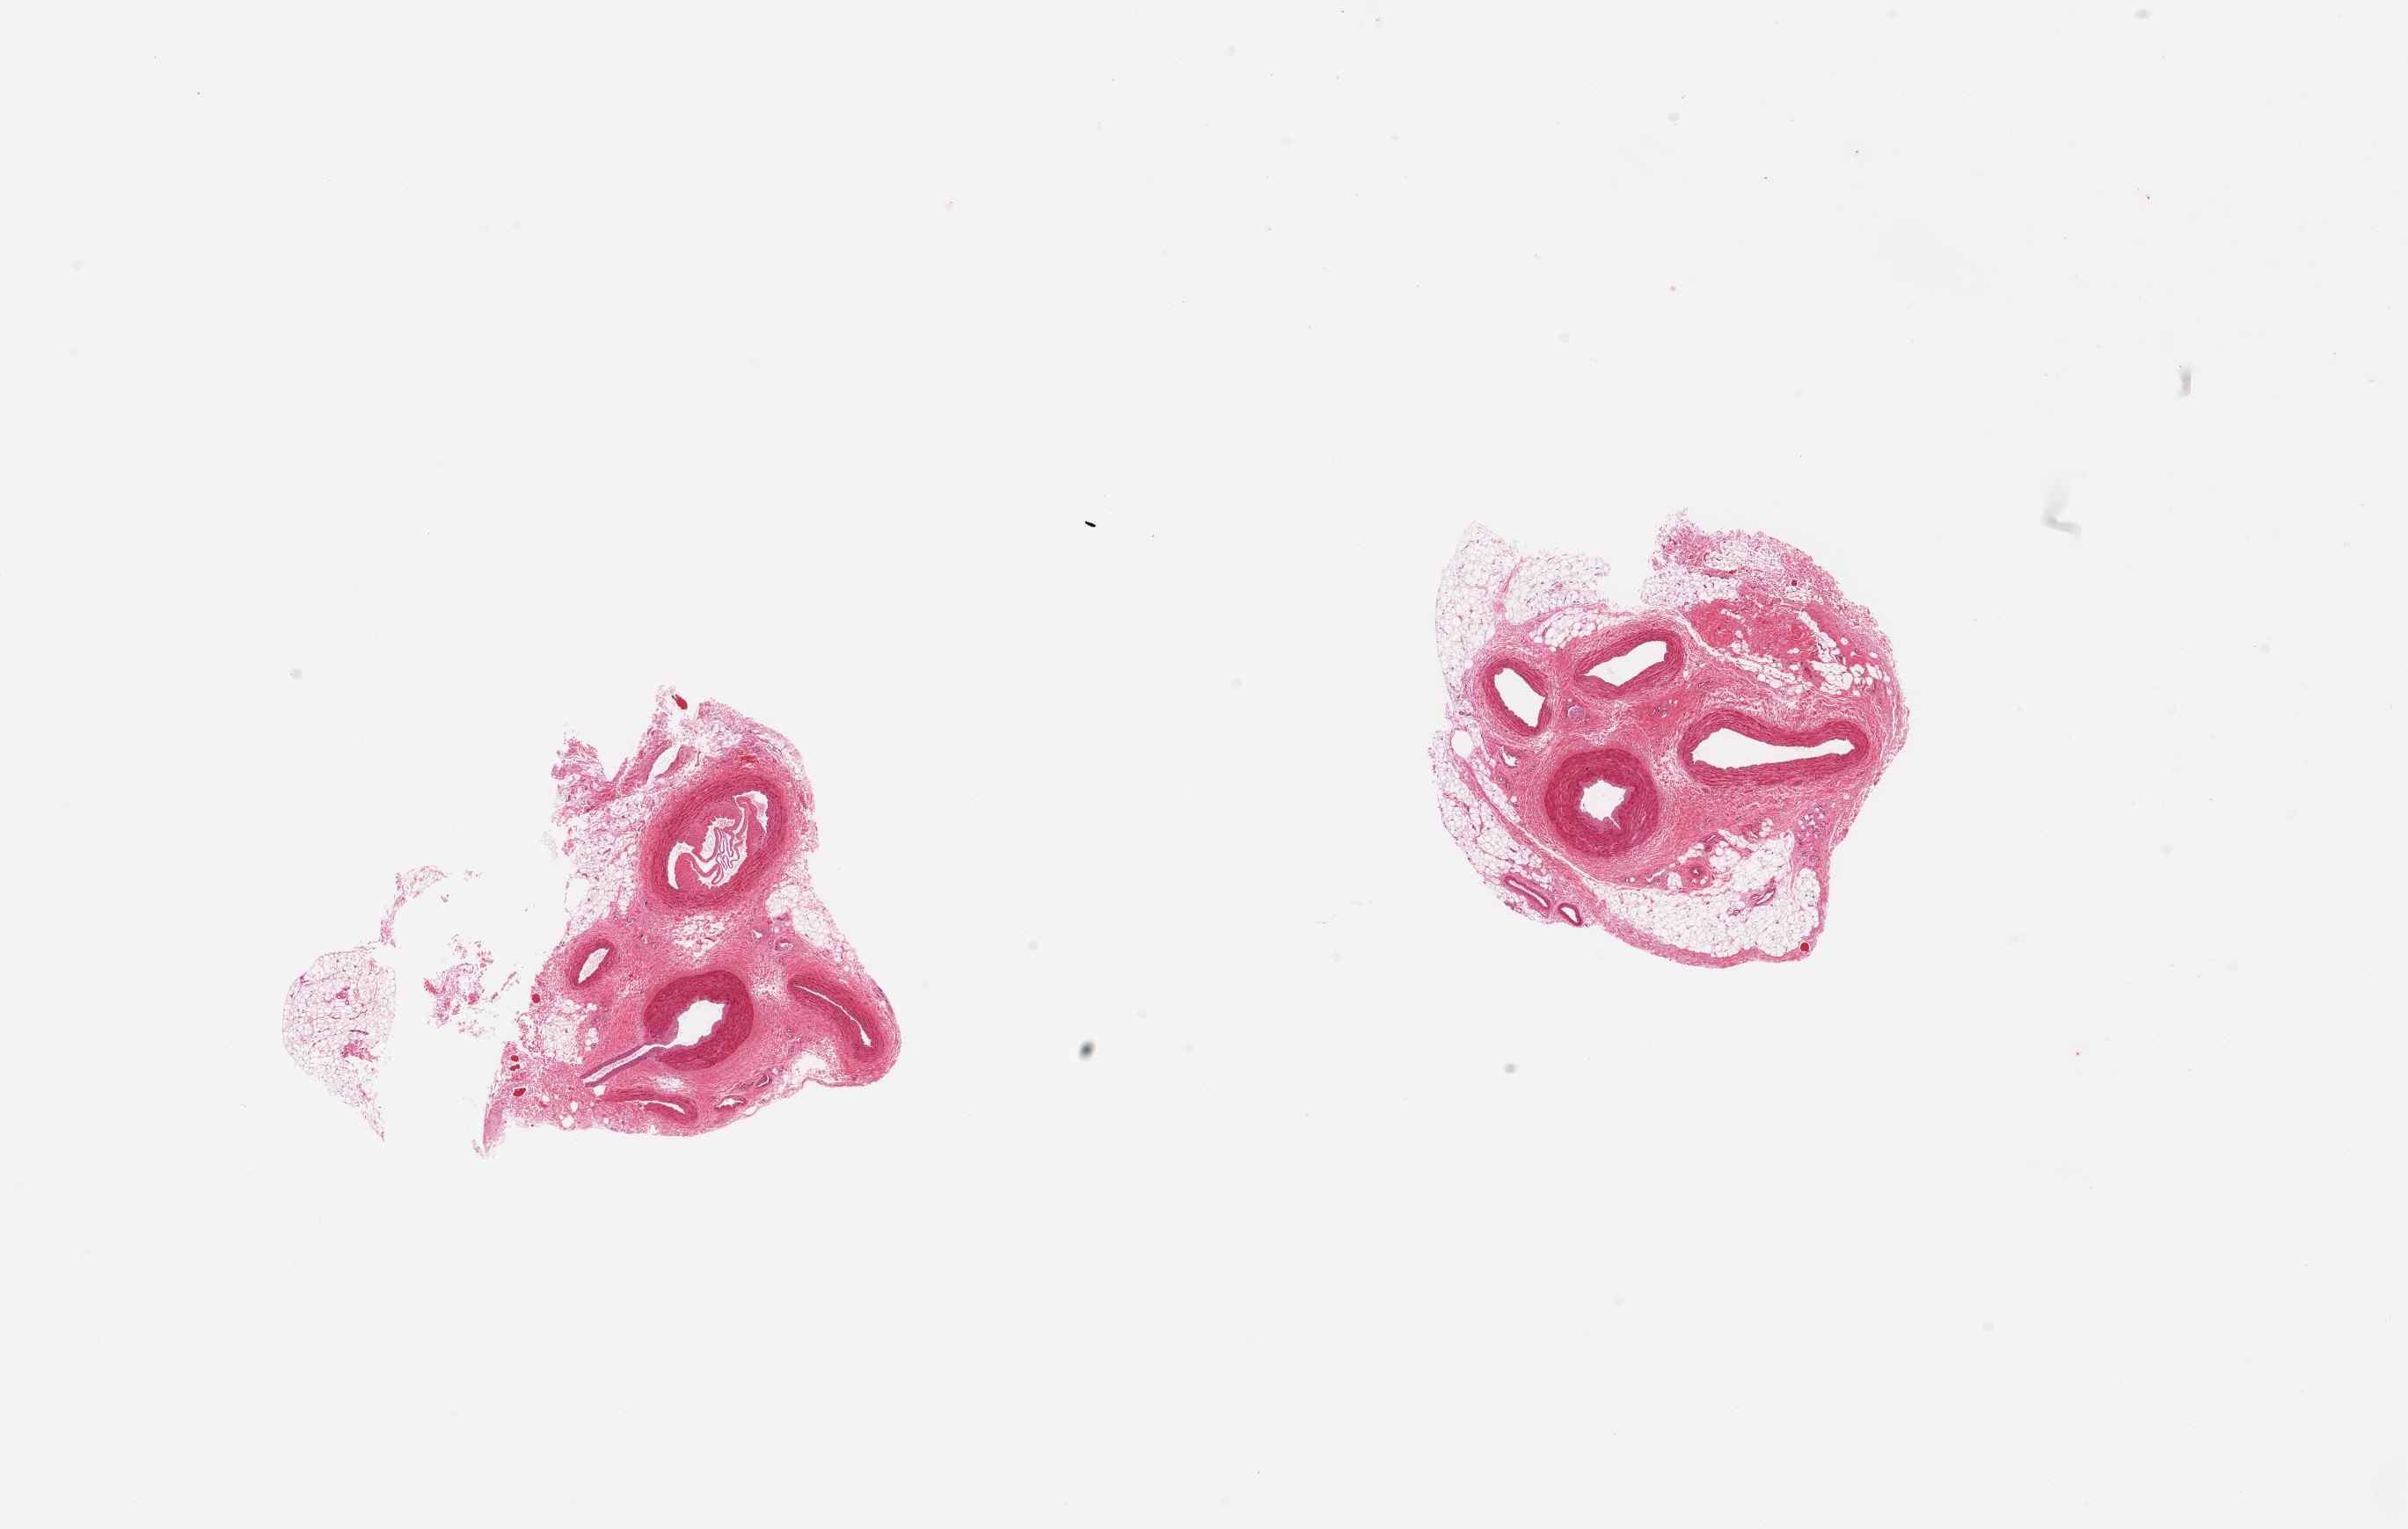
Haematoxylin and eosin whole-slide image, brightfield — a low-resolution overview of the entire scanned area, about 21.7 x 13.8 mm (from a 20x scan); PAXgene-fixed paraffin-embedded (PFPE) section; sampled site (target tissue): tibial artery; tissue donor sample. Donor: female.
Review note (as recorded): 2 pieces, not single artery but aggregate of smaller twigs.